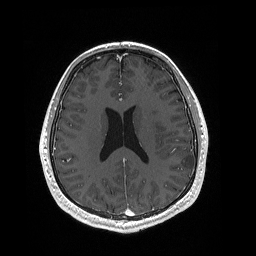
Brain MRI from a brain-tumour surgery series, one axial slice. Position 85 of 192 along the scan axis. T1-weighted post-contrast. 1 mm slice thickness. 256 × 256 image matrix. Case-level facts recorded for this patient, not image findings: histopathology: Dysembryoplastic neuroepithelial tumor; WHO grade: 1; IDH mutation: no; tumour location: Left Inferior Parietal.
Annotated regions visible in this slice (expert manual segmentation):
- tumour: box from (x=180, y=159) to (x=190, y=162) px